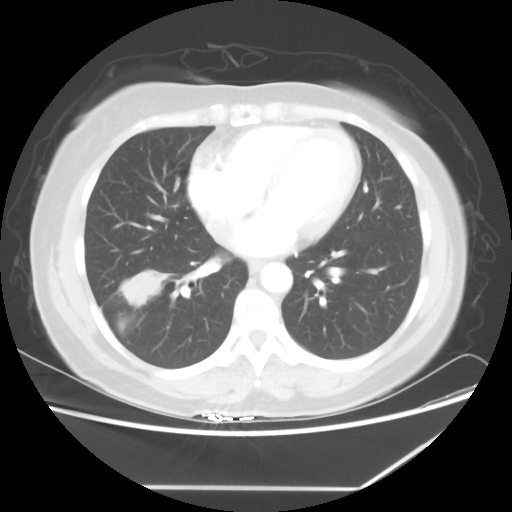
Chest CT, one axial slice; position 25 of 60 along the scan axis; reconstruction kernel STANDARD; 100 kVp; lung window (W 1500 / L -600 HU); 5 mm slice thickness; 512 × 512 image matrix, field of view 374 × 374 mm. Female patient, age 42 years. From the clinical record (not read from this slice): clinical TNM (as recorded): T2 N1 M0.
Structures marked on this image (rectangle marked by the reading radiologist):
- lung tumour (recorded histology: adenocarcinoma): bounding box [x1, y1, x2, y2] px = [114, 265, 170, 315]